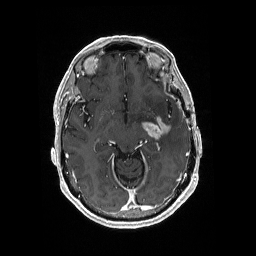
Brain MRI from a brain-tumour surgery series, one axial slice; slice 110 of 176 in the series (ordered by position); T1-weighted post-contrast; 1 mm slice thickness; 256 × 256 image matrix, field of view 256 × 256 mm. Case-level facts recorded for this patient, not image findings: histopathology: Glioblastoma; WHO grade: 4; IDH mutation: no.
Outlined on this slice (outlined manually by an expert reader):
- tumour: bounding box [x1, y1, x2, y2] px = [141, 116, 171, 139]